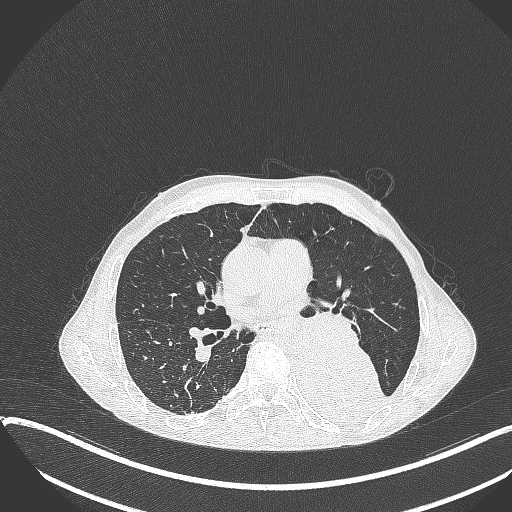
Chest CT, one axial slice; position 200 of 401 along the scan axis; lung window (W 1500 / L -600 HU); 1 mm slice thickness; 512 × 512 image matrix, field of view 400 × 400 mm. Male patient, age 57 years. Case-level facts recorded for this patient, not image findings: clinical TNM (as recorded): T4 N0 M0.
Outlined on this slice (bounding box drawn by a radiologist):
- lung tumour (recorded histology: squamous cell carcinoma): bounding box [x1, y1, x2, y2] px = [289, 334, 382, 428]